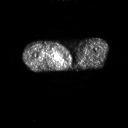
FDG PET of an extremity soft-tissue mass (from a PET/CT study), one axial slice. Position 240 of 311 along the scan axis. 128 × 128 image matrix. Male patient, age 50 years. Case-level facts recorded for this patient, not image findings: histological type: undifferentiated - pleiomorphic; grade: high; site of the primary tumour: right thigh.
Outlined on this slice (expert contour drawn on MRI and transferred to this co-registered scan by the dataset authors):
- gross tumour volume including surrounding oedema: bounding box (x1, y1, x2, y2) in pixels: (41, 49, 56, 60)
- gross tumour volume (mass): (51, 54, 55, 58)